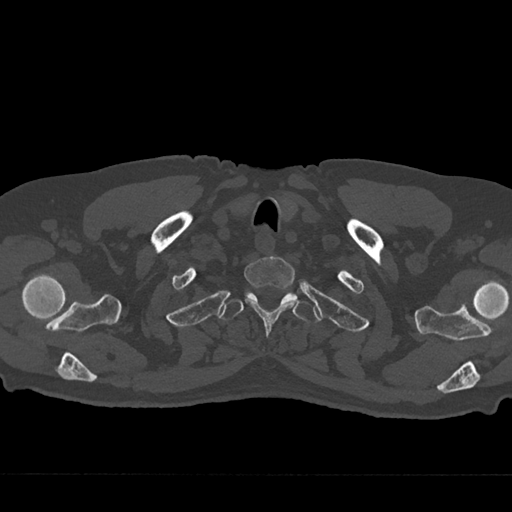
CT including the spine, one axial slice. Position 638 of 797 along the scan axis. Reconstruction kernel Br40s/3. Bone window (W 1800 / L 400 HU). 0.5 mm slice thickness. 512 × 512 image matrix. Male patient, age 75 years. From the clinical record (not read from this slice): primary cancer: renal; vertebrae with lytic lesions (as recorded): T4.
Structures marked on this image (semi-automatically segmented with operator editing):
- T1 vertebra: bounding box <244,256,298,337> (left, top, right, bottom; pixels)
- T2 vertebra: <218,292,320,324>